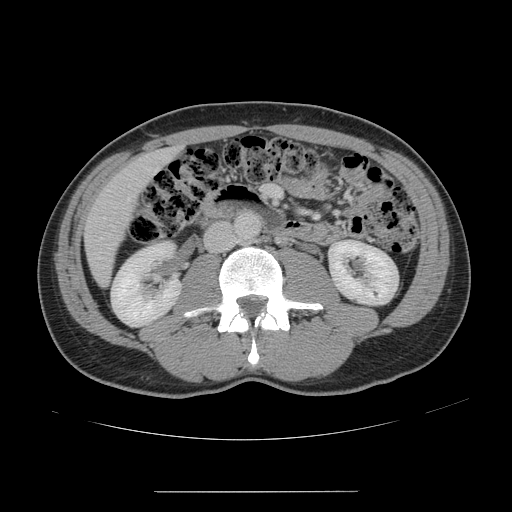
Contrast-enhanced abdominal CT, one axial slice. Slice 44 of 178 in the series (ordered by position). Intravenous contrast given. Soft-tissue window (W 400 / L 40 HU). 2.5 mm slice thickness. 512 × 512 image matrix, field of view 401 × 401 mm. Male patient, age 53 years. Case-level facts recorded for this patient, not image findings: diagnosis: colorectal cancer liver metastases, imaged before liver resection; multiple liver metastases: yes.
Annotated regions visible in this slice (expert manual segmentation):
- hepatic veins: box from (x=97, y=171) to (x=155, y=259) px
- liver: (x=85, y=149)–(x=176, y=285)